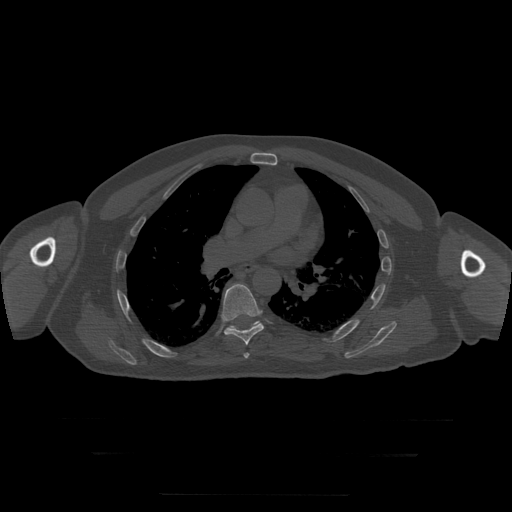
CT including the spine, one axial slice. Slice 185 of 397 in the series (ordered by position). Bone window (W 1800 / L 400 HU). 512 × 512 image matrix, field of view 510 × 510 mm. Patient age 73 years. From the clinical record (not read from this slice): primary cancer: prostate.
Outlined on this slice (semi-automatic segmentation, software-assisted and operator-edited):
- T6 vertebra: bounding box [x1, y1, x2, y2] px = [244, 353, 249, 359]
- T7 vertebra: [222, 284, 264, 346]
- T8 vertebra: [228, 321, 260, 330]